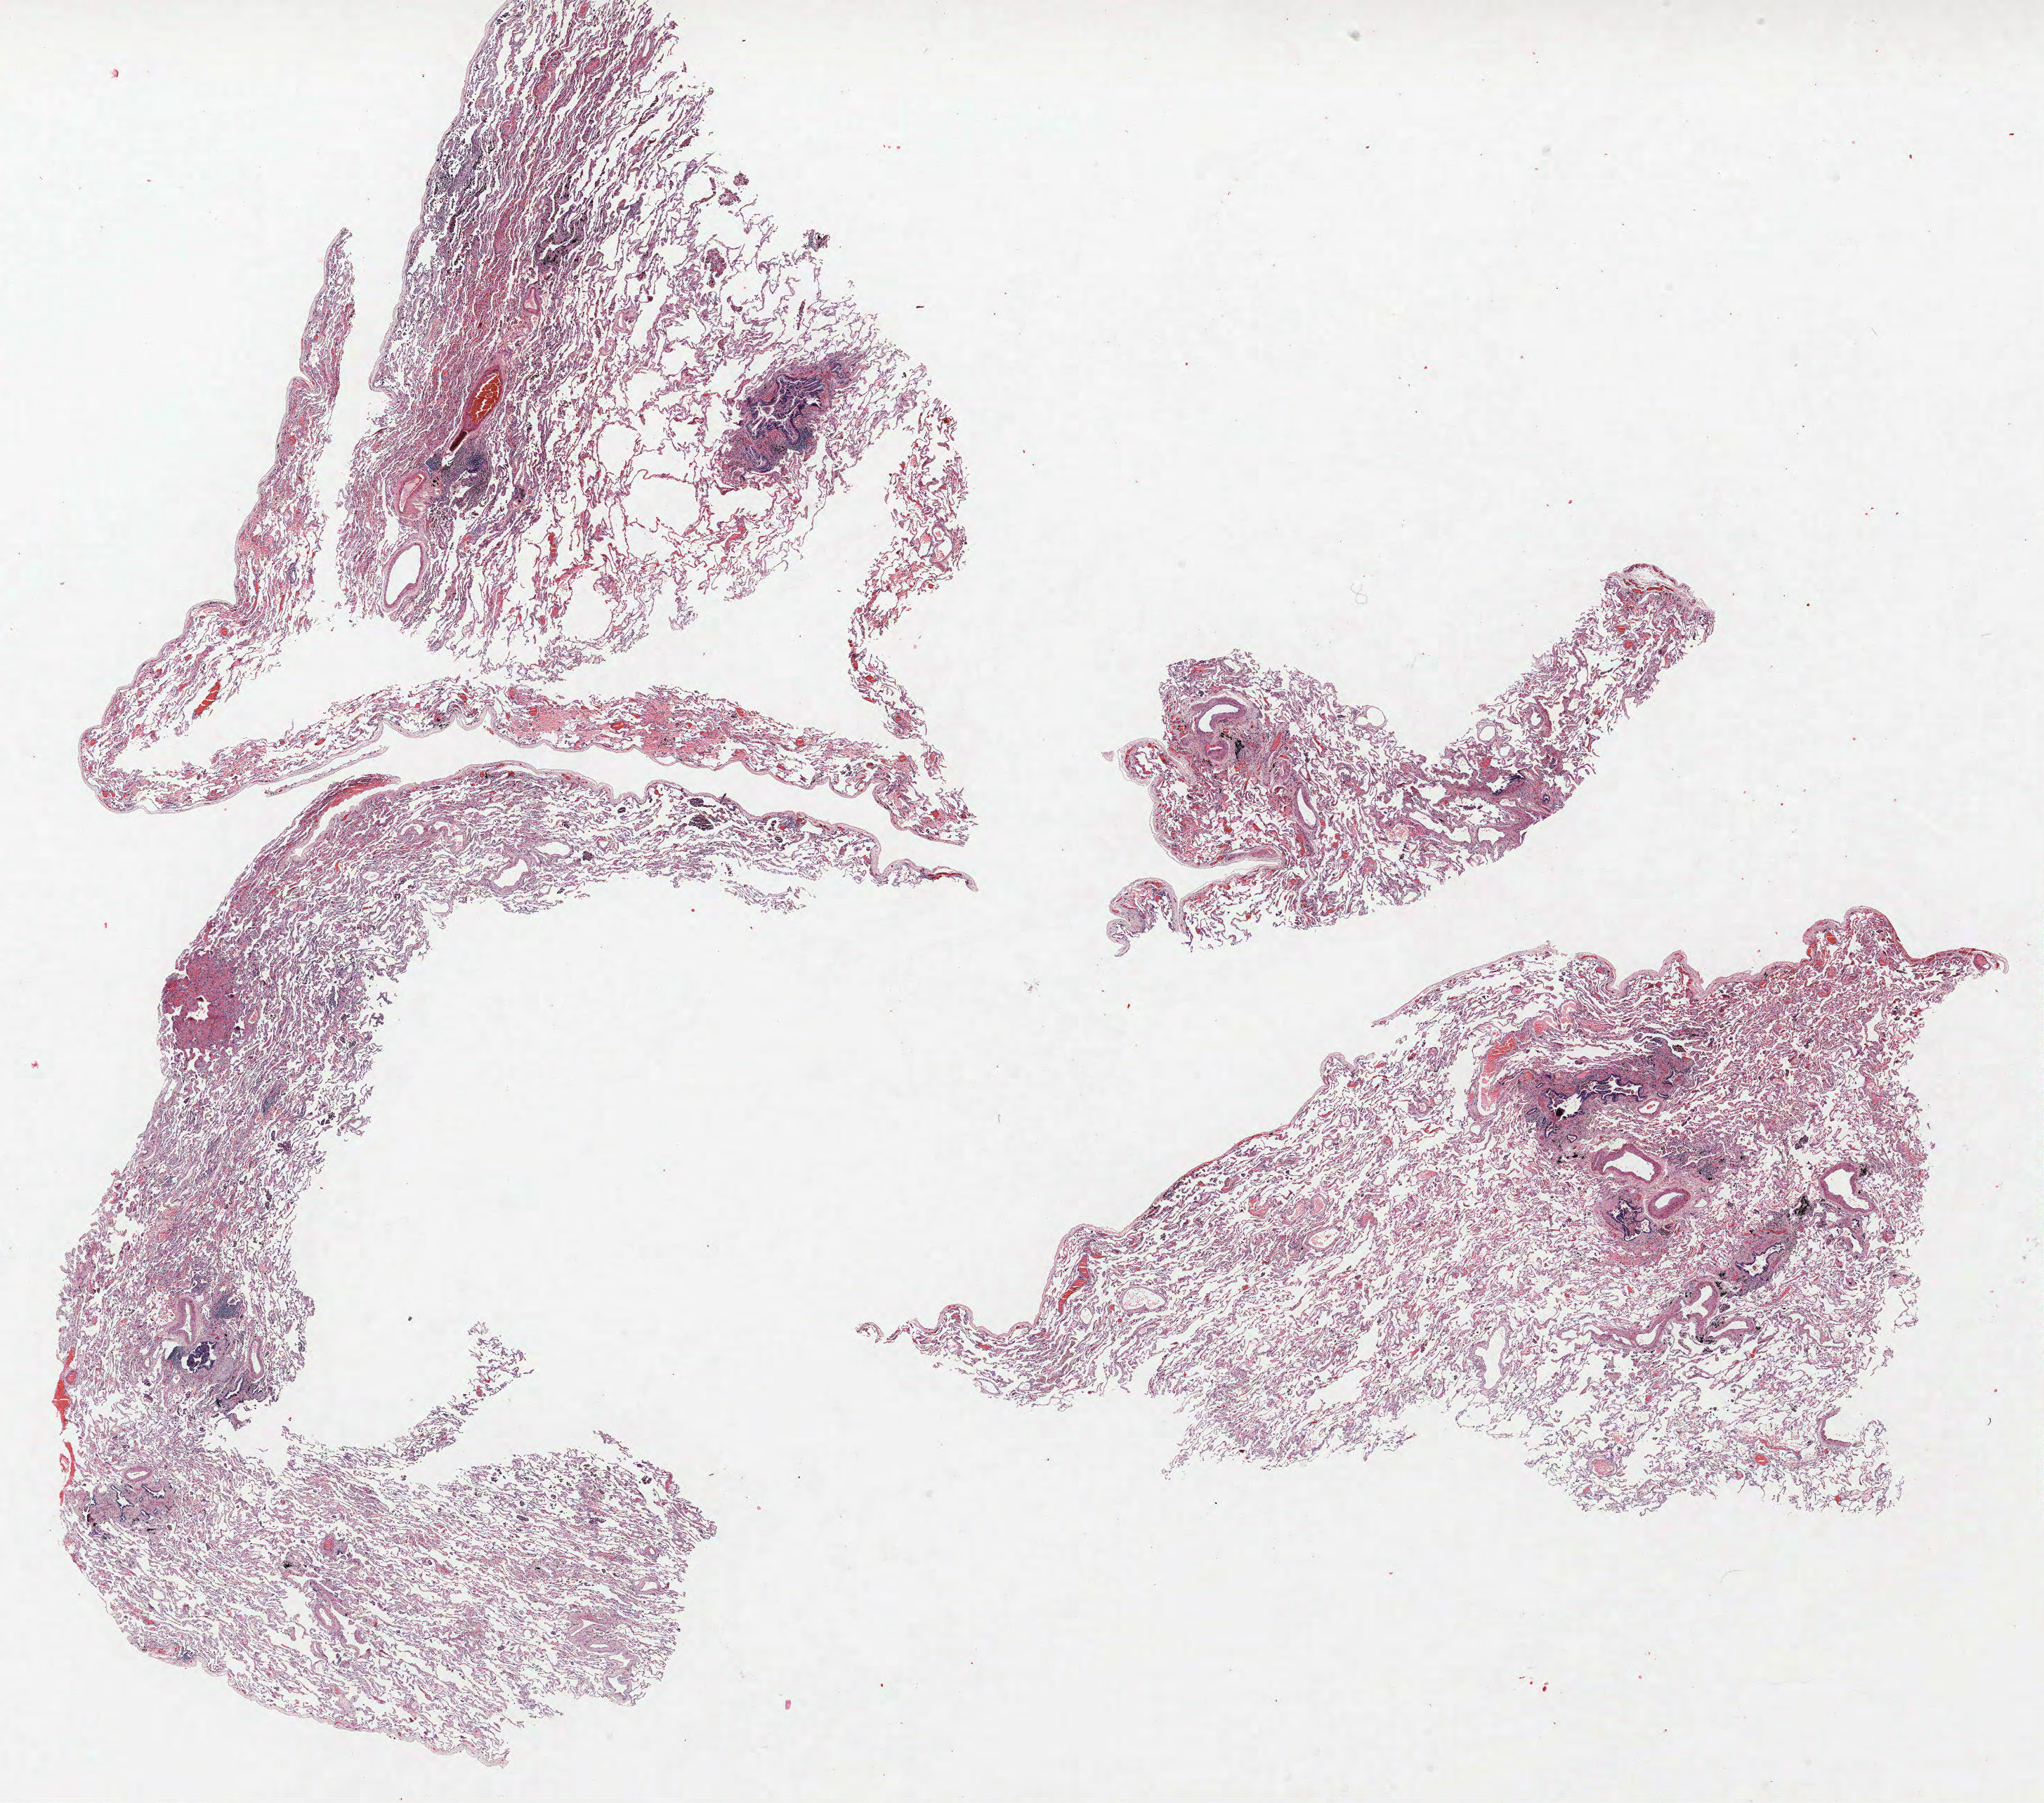
Whole-slide histology image, H&E-stained, whole scanned area (about 23.3 x 20.5 mm, acquisition: 40x scan) shown as a low-resolution overview; FFPE section; lung. Female patient, aged 64 at enrolment. Grade: well differentiated (G1).
* primary tumour location (clinical record): right lower lobe
* tumour size (pathology): 20 mm
* participant's lung-cancer diagnosis: Bronchiolo-alveolar carcinoma, non-mucinous (ICD-O-3 8252/3)
* stage (AJCC 6th edition): IA